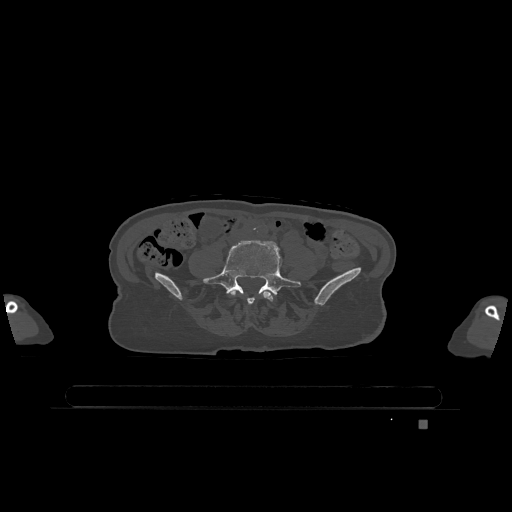
CT including the spine, one axial slice; position 253 of 1317 along the scan axis; bone window (W 1800 / L 400 HU); 512 × 512 image matrix, field of view 500 × 500 mm. Patient: female, 74 years. From the clinical record (not read from this slice): primary cancer: lung; vertebrae with lytic lesions (as recorded): T1, T4, T5, T6, L4, L5.
Annotated regions visible in this slice (semi-automatically segmented with operator editing):
- L4 vertebra: bounding box [x1, y1, x2, y2] px = [230, 291, 273, 302]
- L5 vertebra: [204, 240, 301, 304]